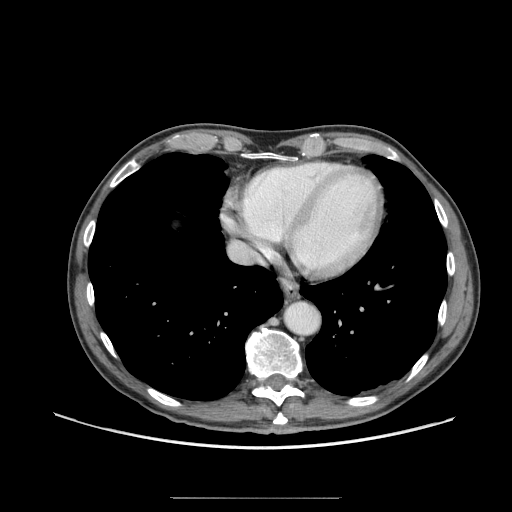
Contrast-enhanced abdominal CT (liver protocol), one axial slice; slice 68 of 71 in the series (ordered by position); reconstruction kernel STANDARD; soft-tissue window (W 400 / L 40 HU); 2.5 mm slice thickness; 512 × 512 image matrix, field of view 400 × 400 mm. From the clinical record (not read from this slice): diagnosis: hepatocellular carcinoma (patient treated with transarterial chemoembolisation; whether this scan precedes or follows treatment is not stated here); TNM stage (as recorded): Stage-I; Child-Pugh class: A; tumour differentiation: well differentiated; tumour nodularity: uninodular.
Annotated regions visible in this slice (semi-automatic segmentation, software-assisted and operator-edited):
- abdominal aorta: bounding box [x1, y1, x2, y2] px = [285, 303, 319, 335]